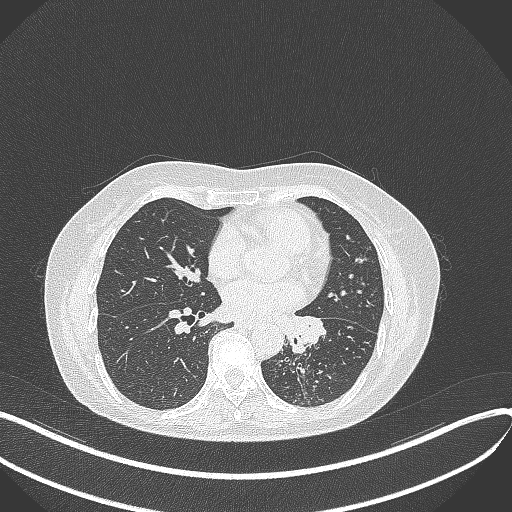
Chest CT, one axial slice. Reconstruction kernel B70f. 100 kVp. Lung window (W 1500 / L -600 HU). 512 × 512 image matrix, field of view 400 × 400 mm. Female patient, age 63 years. Case-level facts recorded for this patient, not image findings: clinical TNM (as recorded): T1b N0 M0; histopathological grade: G2-3.
Outlined on this slice (rectangle marked by the reading radiologist):
- lung tumour (recorded histology: adenocarcinoma): bounding box (x1, y1, x2, y2) in pixels: (285, 311, 336, 356)